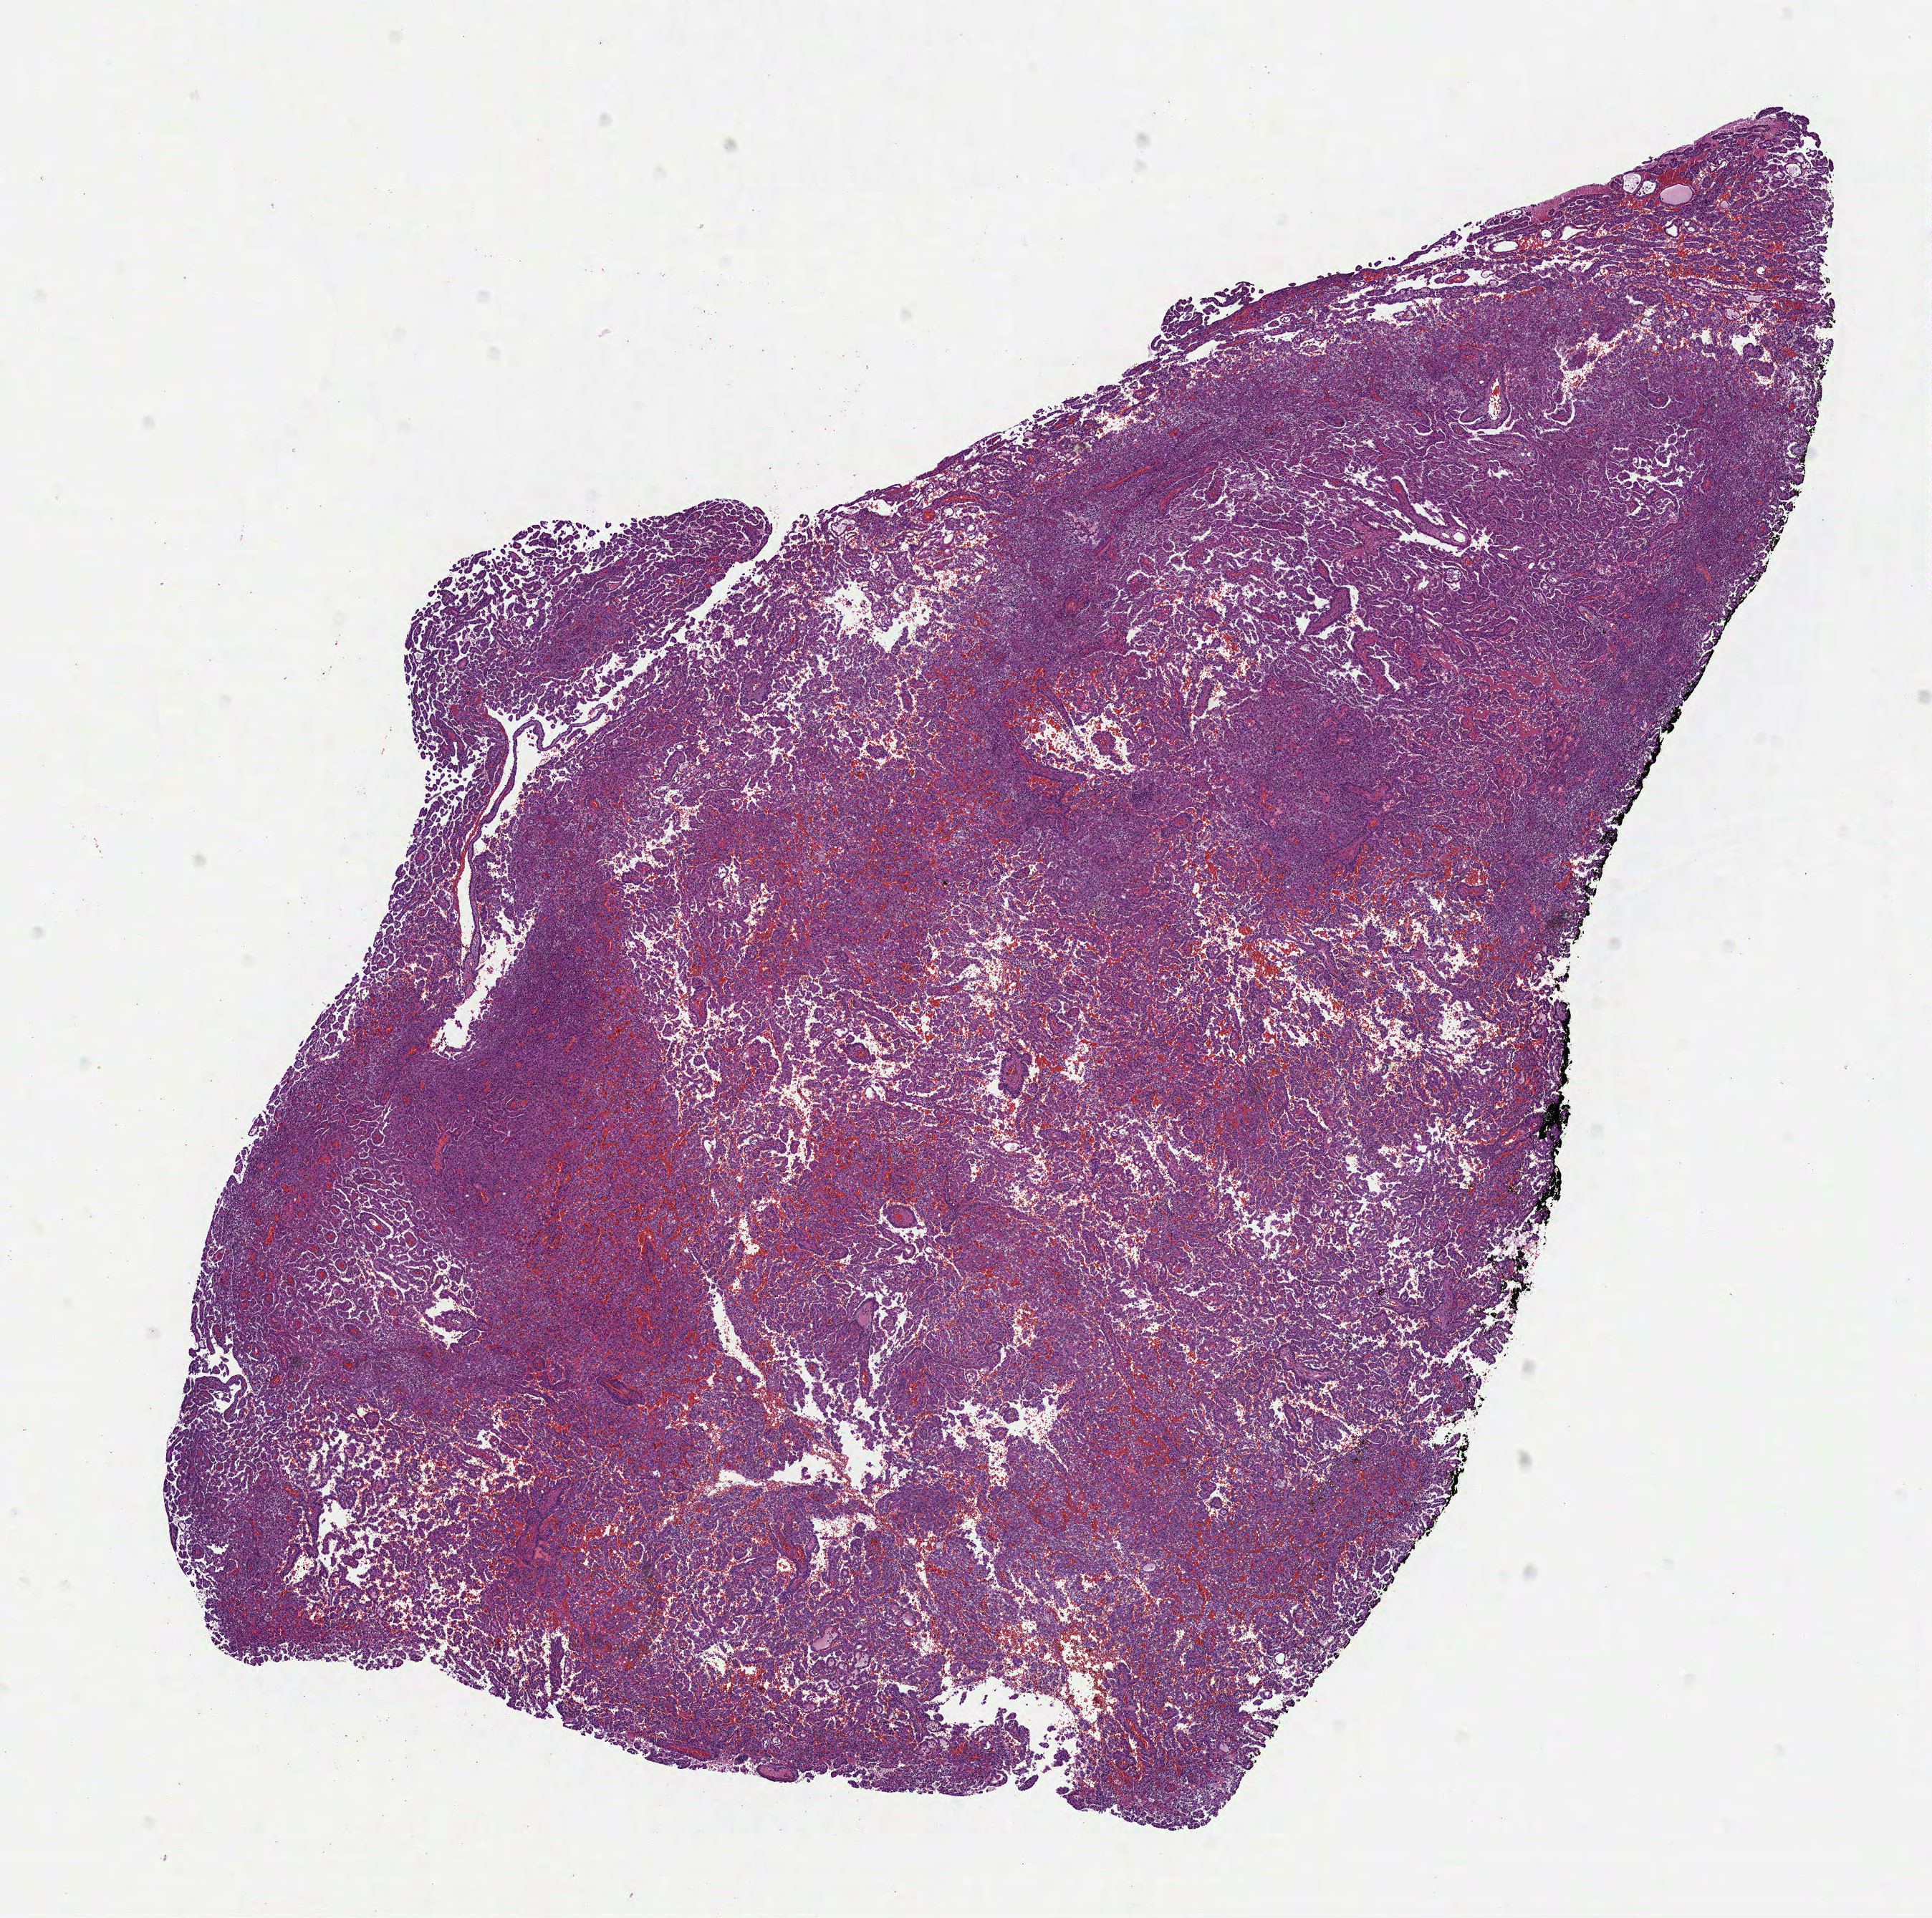
Digitized H&E-stained tissue section (whole slide) — a low-resolution overview of the entire scanned area, about 10.9 x 10.8 mm (slide scanned at 40x), formalin-fixed paraffin-embedded (FFPE) diagnostic section, sample: primary tumour, kidney. Male, age 67 years at initial diagnosis.
Diagnosis: Papillary adenocarcinoma, NOS. AJCC pathologic stage: I (7th edition). Laterality: left.